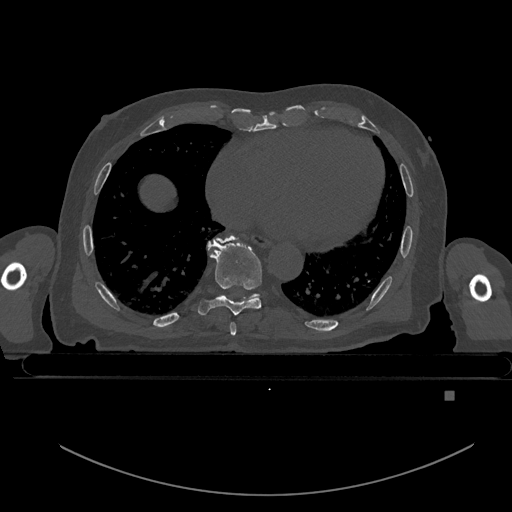
CT including the spine, one axial slice; slice 197 of 969 in the series (ordered by position); bone window (W 1800 / L 400 HU); 0.5 mm slice thickness; 512 × 512 image matrix. Male patient, age 82 years. Case-level facts recorded for this patient, not image findings: primary cancer: prostate.
Structures marked on this image (semi-automatic segmentation, software-assisted and operator-edited):
- T7 vertebra: bounding box [x1, y1, x2, y2] px = [230, 322, 236, 336]
- T8 vertebra: [198, 237, 269, 315]
- T9 vertebra: [216, 235, 259, 299]